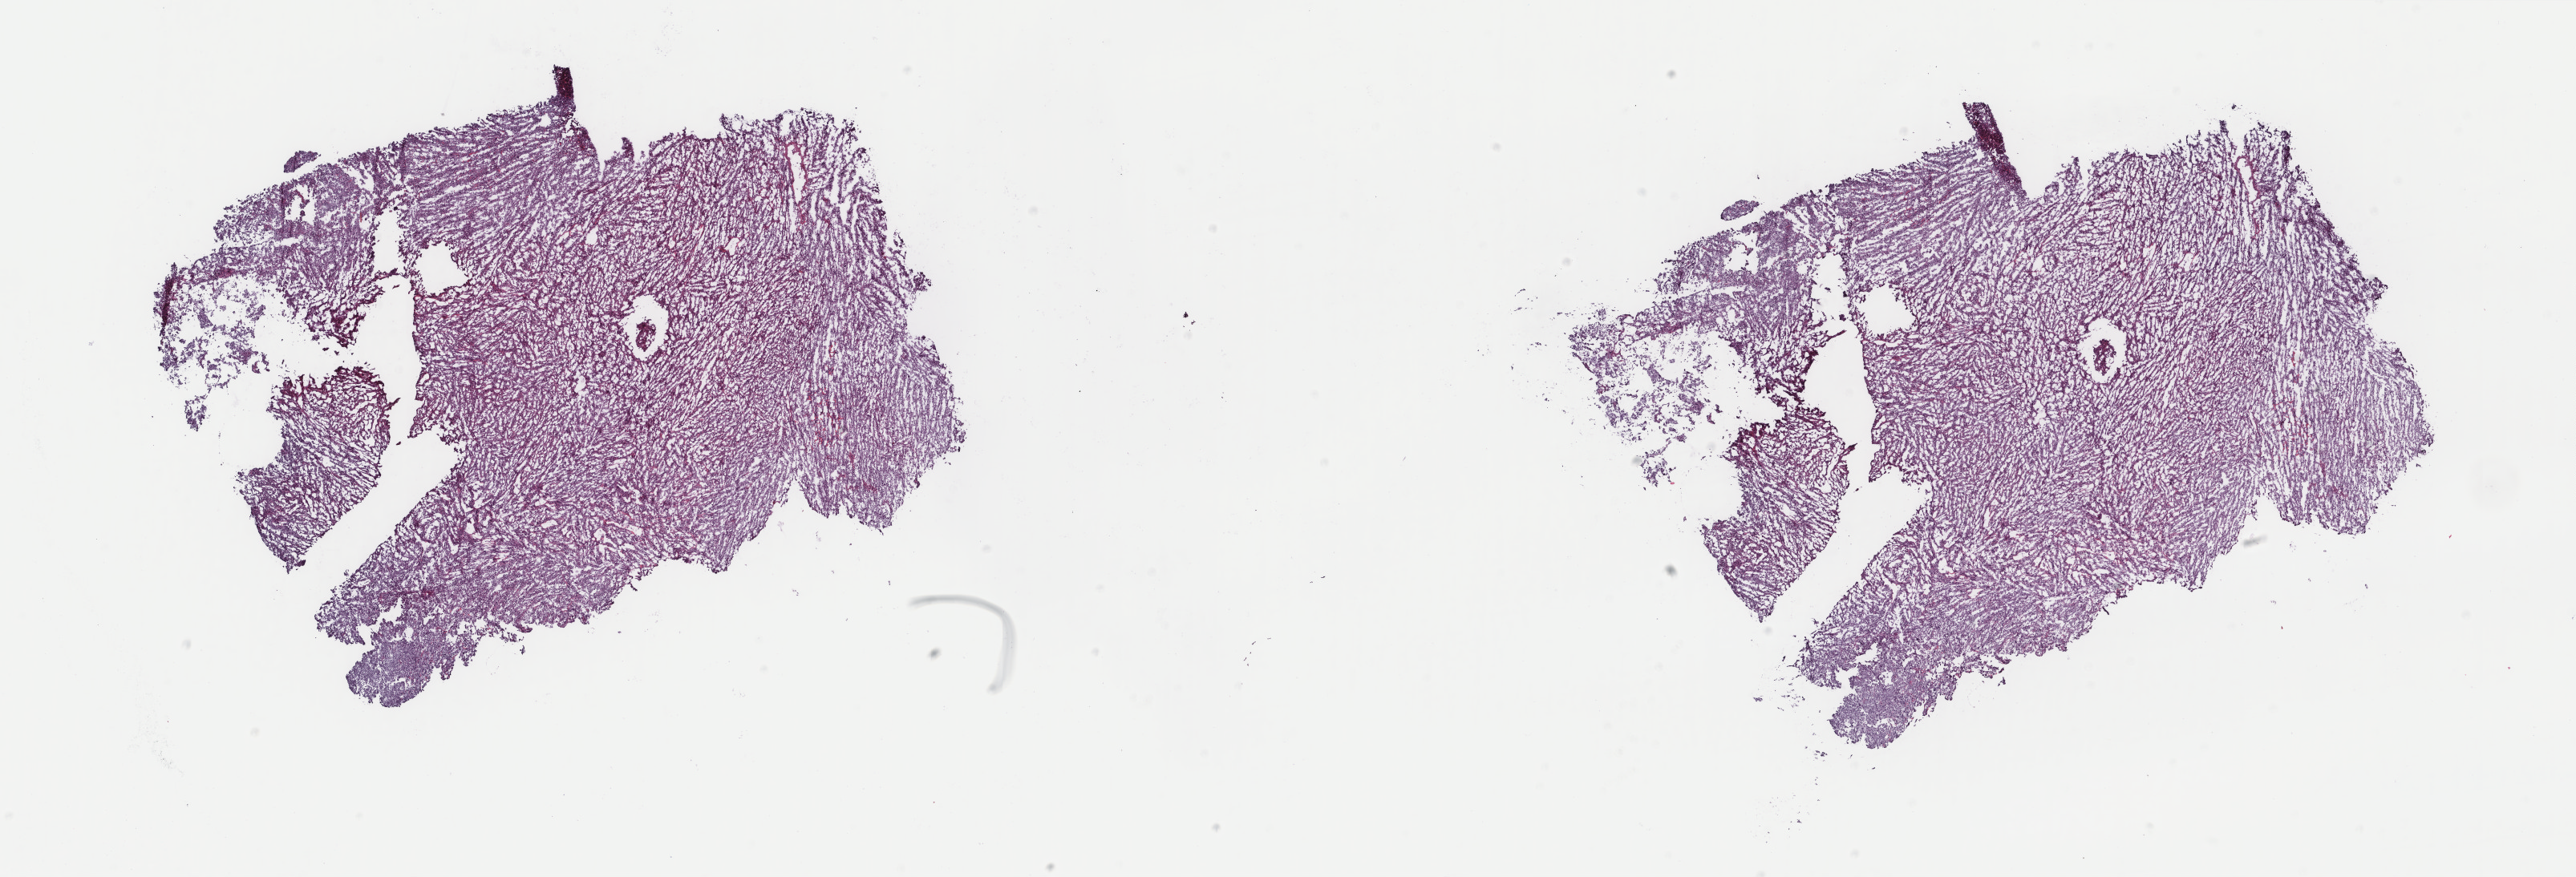
Whole-slide histology image, H&E — whole scanned area (about 25.5 x 8.7 mm, from a 40x scan) shown as a low-resolution overview; frozen section from the top of the tissue portion; sample: primary tumour, uterus. Patient: female, age at initial diagnosis 63 years. Composition of this section per pathologist review: tumour cells 100%, tumour nuclei 95%, normal cells 0%, stromal cells 0%, necrosis 0%. Inflammatory infiltration, as recorded: lymphocyte infiltration 0%, monocyte infiltration 0%, neutrophil infiltration 0%.
Diagnosis: Leiomyosarcoma, NOS.